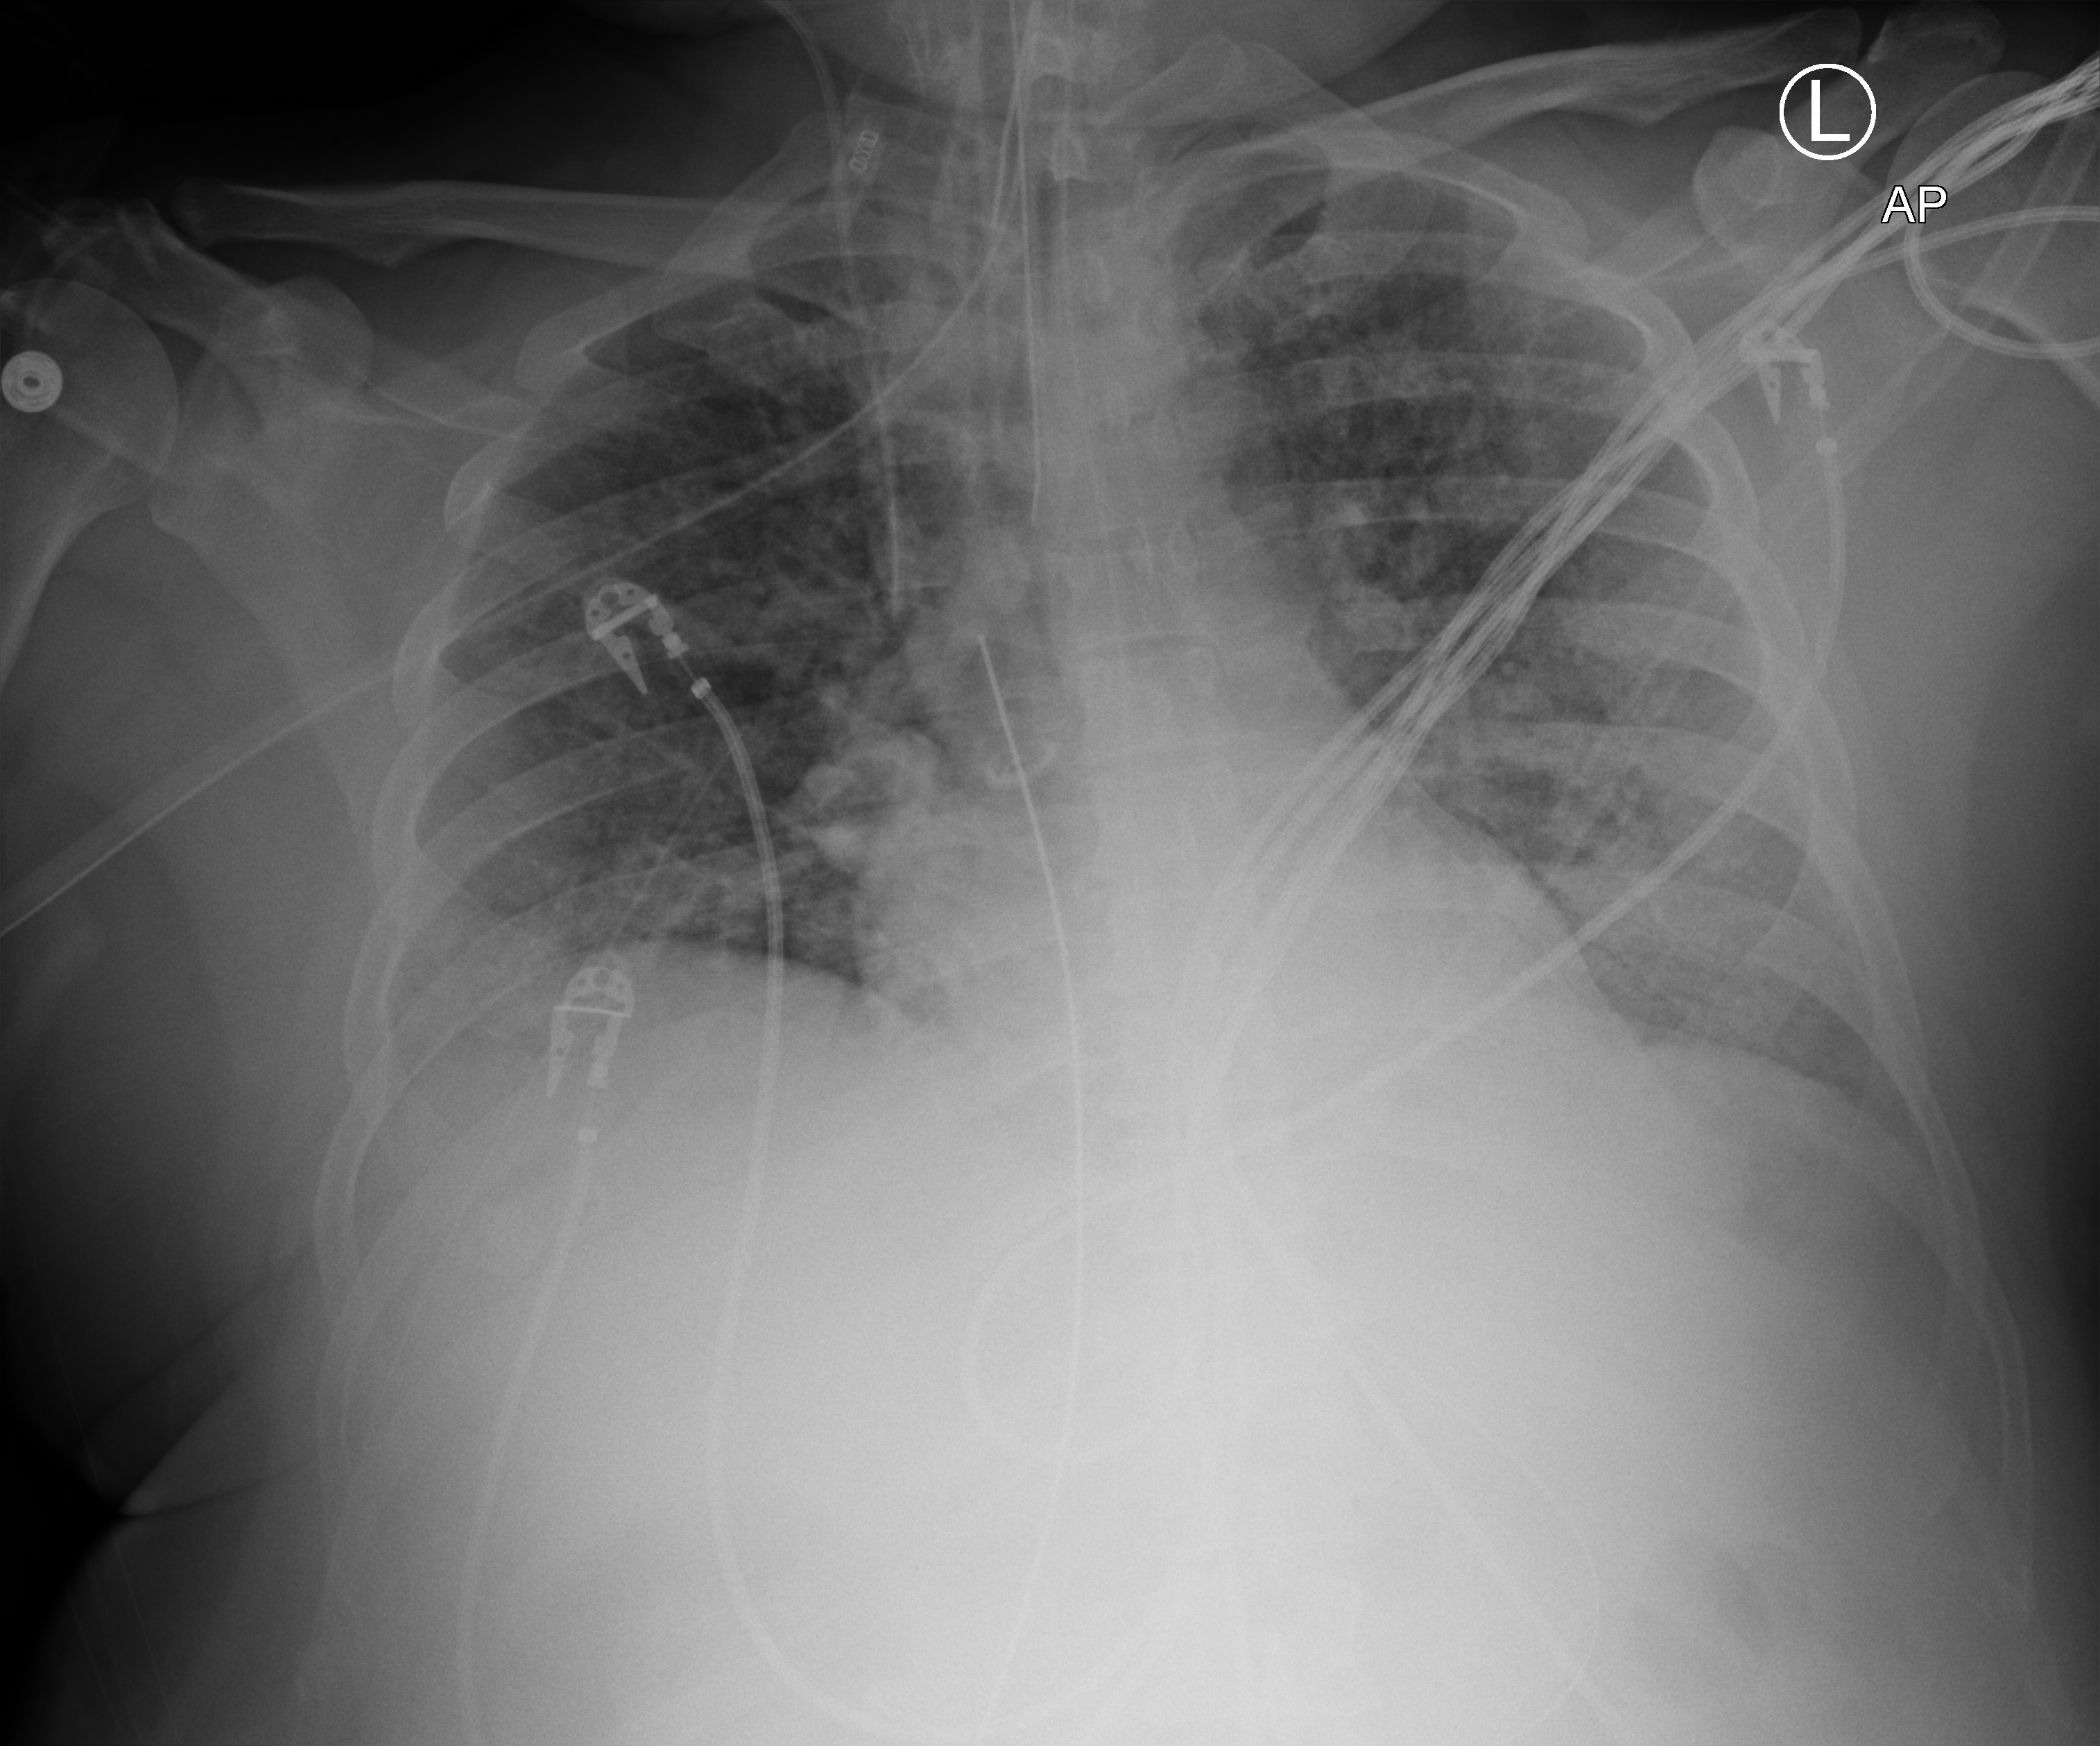
Chest X-ray (portable); anteroposterior (AP) projection. Patient hospitalised with COVID-19; male, aged 18–59 years.
Admission-level facts for this patient (not findings on this image; timing relative to this image not recorded):
- admitted to intensive care during this hospital stay: yes
- COPD (admission record): no